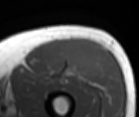
MRI of an extremity soft-tissue mass, one axial slice; slice 43 of 86 in the series (ordered by position); MR volume resampled by the dataset authors to the PET/CT grid (not the native acquisition matrix); 3.27 mm slice thickness; 139 × 117 image matrix, field of view 136 × 114 mm. Male patient. Case-level facts recorded for this patient, not image findings: histological type: extraskeletal osteosarcoma; grade: high; site of the primary tumour: thigh.
Annotated regions visible in this slice (expert contour drawn on MRI and transferred to this co-registered scan by the dataset authors):
- gross tumour volume (mass): box from (x=56, y=39) to (x=101, y=76) px